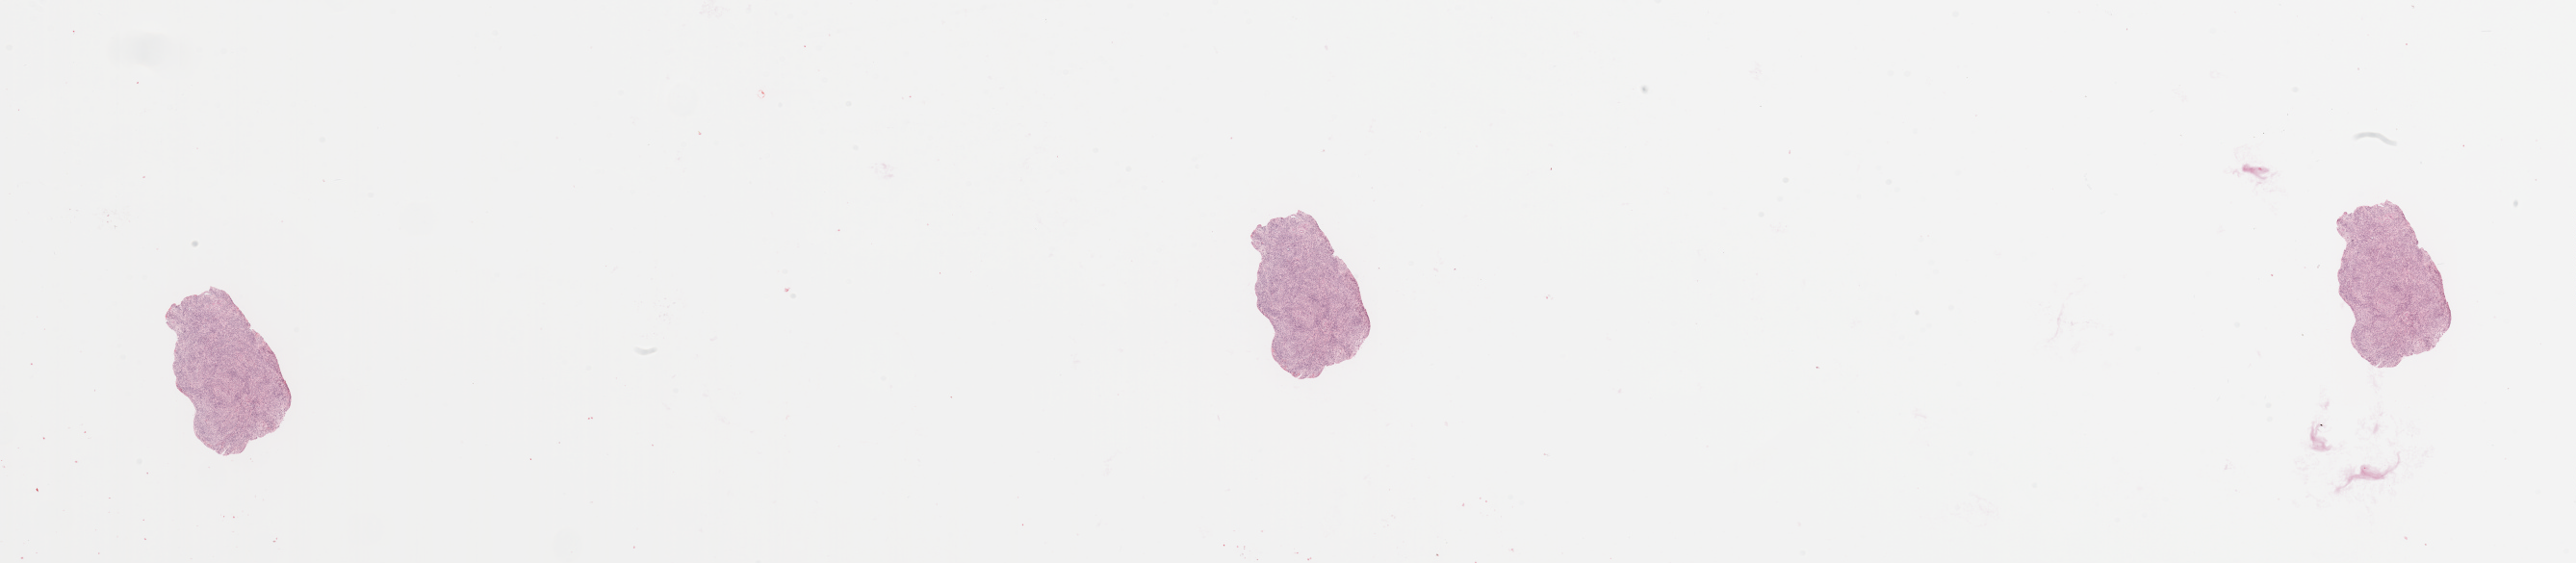
Hematoxylin and eosin (H&E) stained whole-slide image, whole scanned area (about 42.3 x 9.3 mm) shown as a low-resolution overview. Uterus, normal (non-tumour) tissue. Patient: female, age 69 years.
- this section: normal (non-tumour) tissue from the same patient
- patient diagnosis: Endometrioid adenocarcinoma, NOS